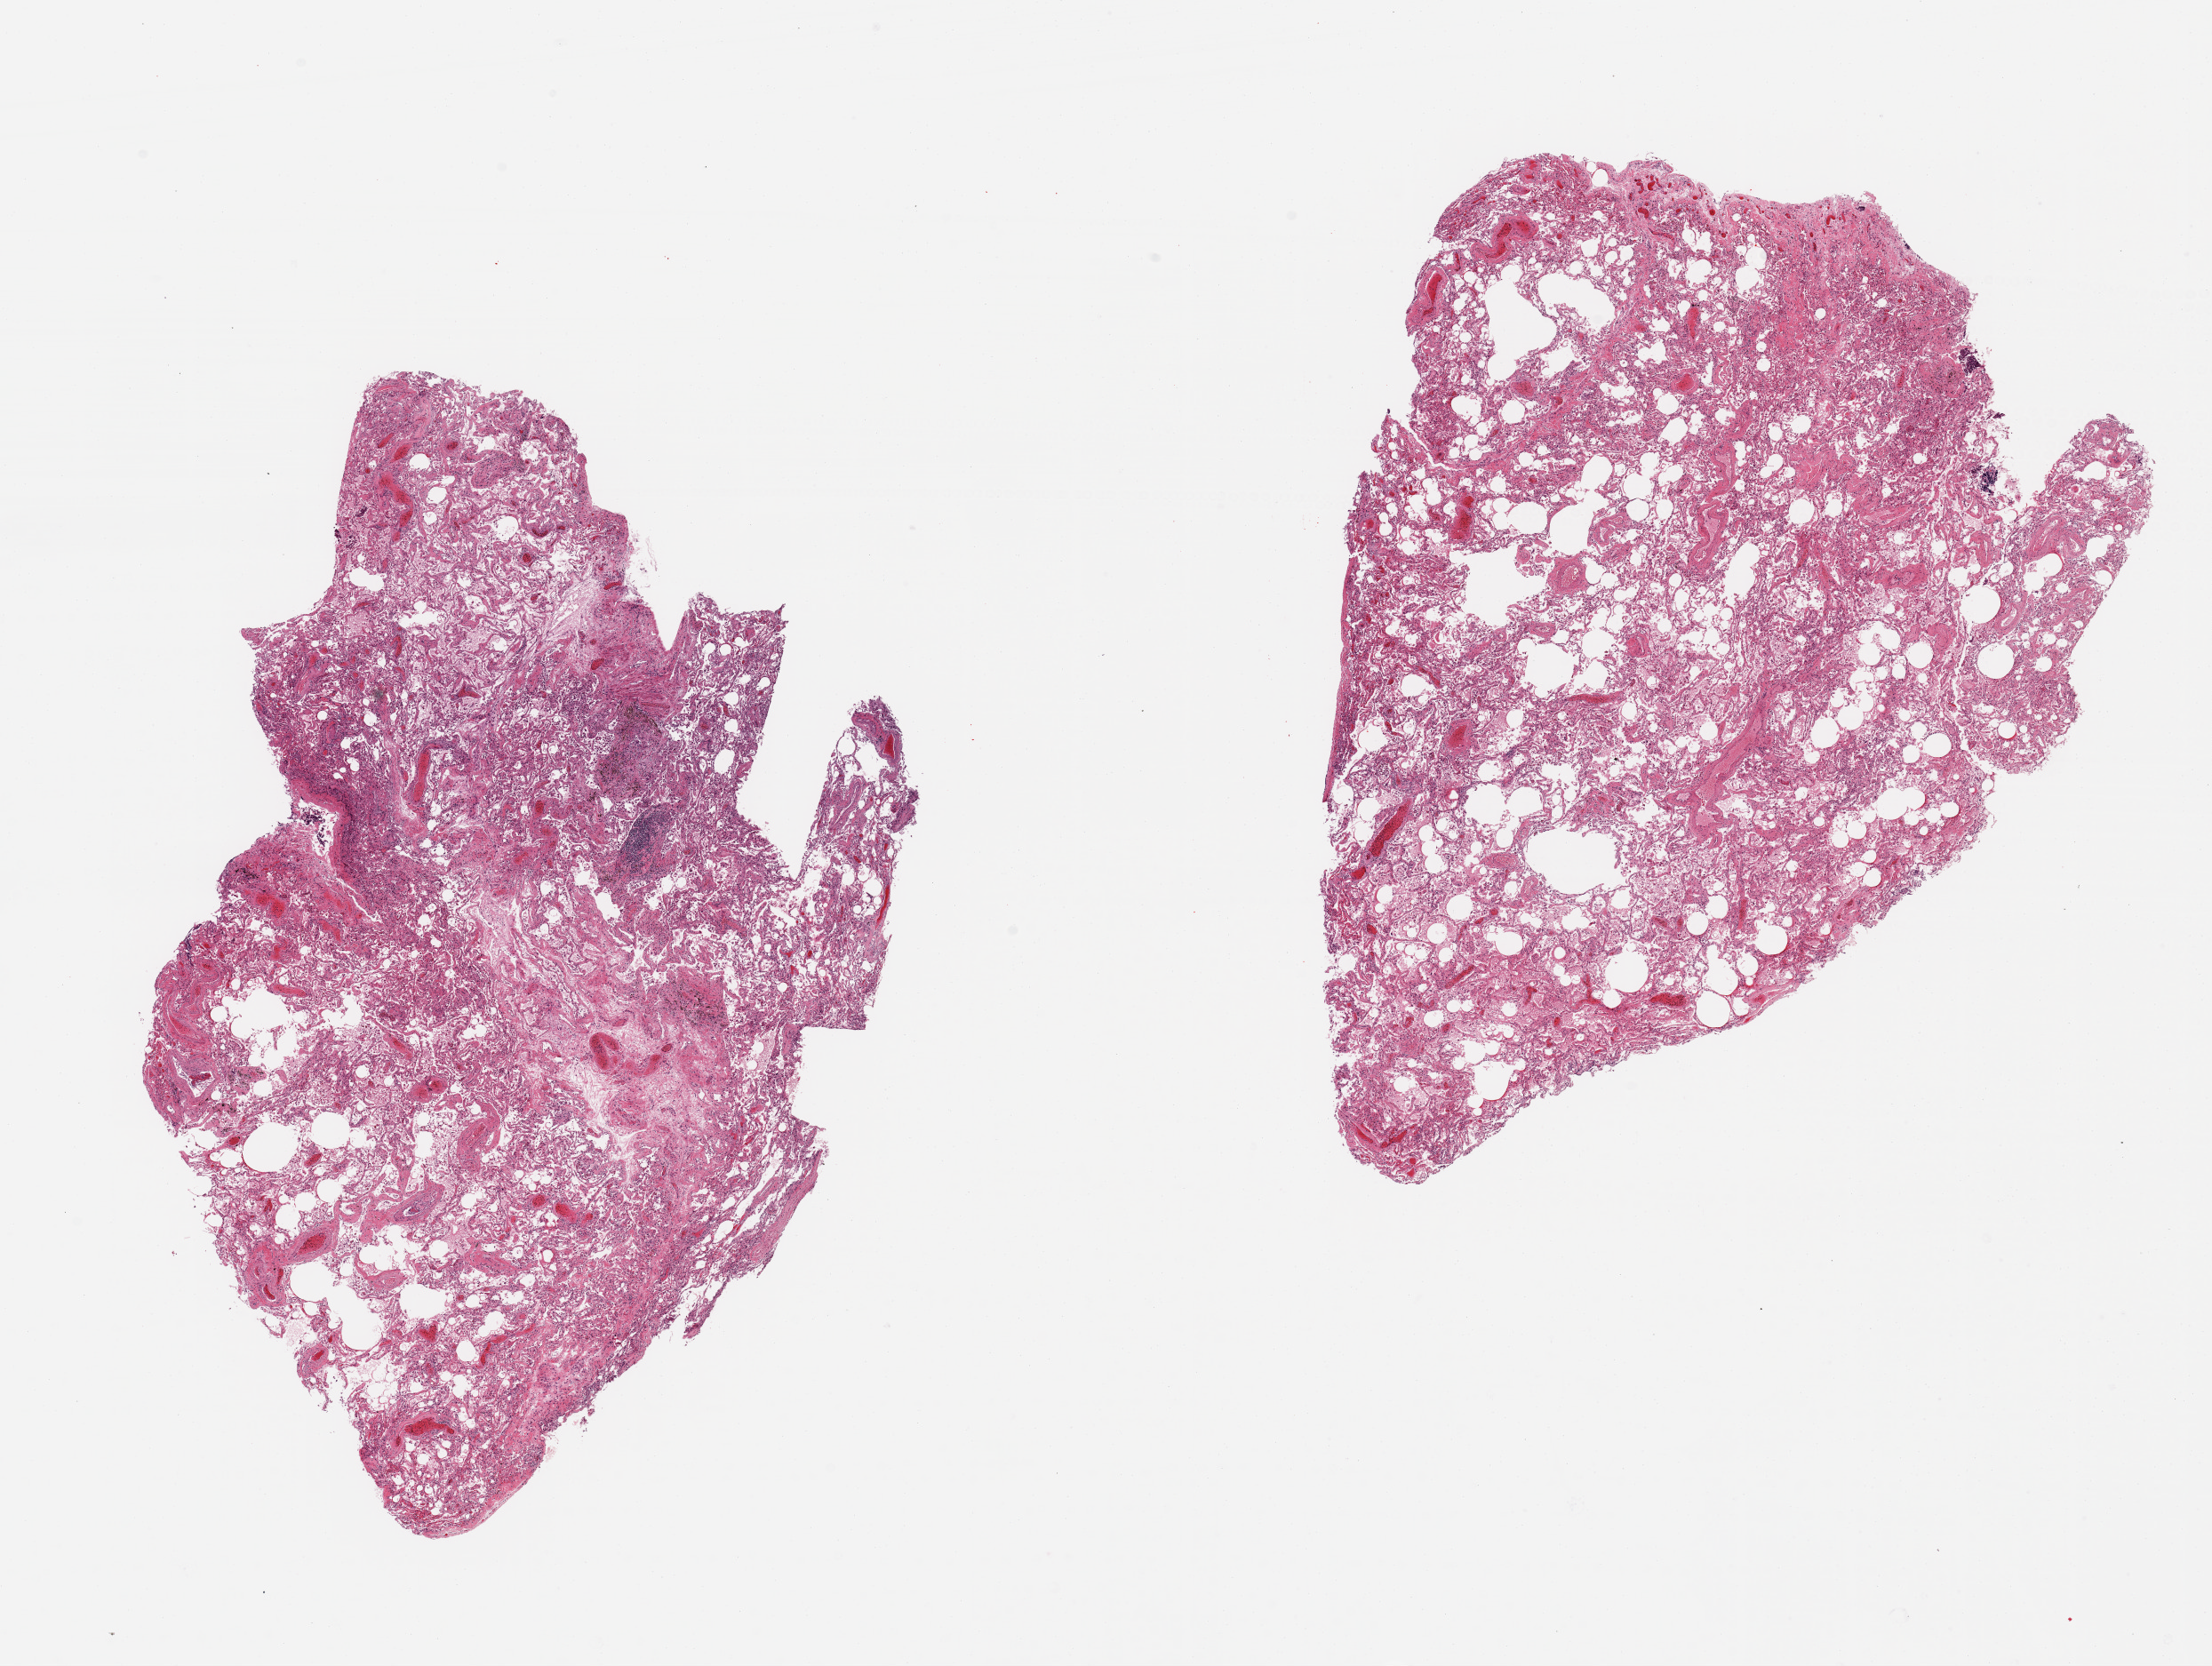
Haematoxylin and eosin whole-slide image, shown as a low-resolution overview of the whole scanned area (about 19.7 x 14.8 mm), PAXgene-fixed, paraffin-embedded tissue, sampled site (target tissue): lung, donor tissue sample. Donor sex: female.
Review note (as recorded): 2 pieces, moderate congestion.